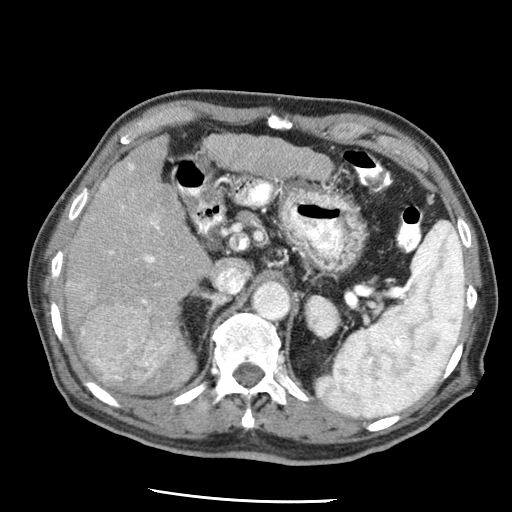
Contrast-enhanced abdominal CT (liver protocol), one axial slice. Position 31 of 79 along the scan axis. Soft-tissue window (W 400 / L 40 HU). 2.5 mm slice thickness. 512 × 512 image matrix, field of view 320 × 320 mm. Case-level facts recorded for this patient, not image findings: diagnosis: hepatocellular carcinoma (patient treated with transarterial chemoembolisation; whether this scan precedes or follows treatment is not stated here); TNM stage (as recorded): Stage-IIIA; Child-Pugh class: A.
Outlined on this slice (semi-automatic segmentation, software-assisted and operator-edited):
- liver parenchyma outside the tumour (the mass and vessels are separate outlines, so this box may not span the whole liver): box from (x=64, y=136) to (x=210, y=386) px
- mass: (x=65, y=271)–(x=171, y=389)
- liver vessels: (x=103, y=163)–(x=173, y=346)